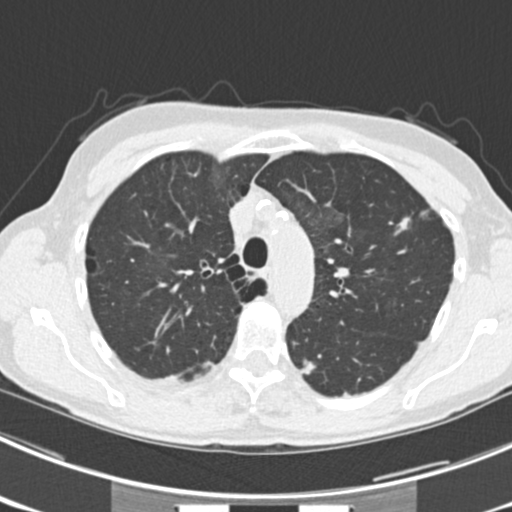
Low-dose screening chest CT, one axial slice. Position 166 of 225 along the scan axis. 120 kVp. Lung window (W 1500 / L -600 HU). 2 mm slice thickness. 512 × 512 image matrix, field of view 302 × 302 mm.
Structures marked on this image (expert manual segmentation):
- lesion 2 (tumor, lower lobe of left lung): bounding box (x1, y1, x2, y2) in pixels: (300, 357, 316, 376)